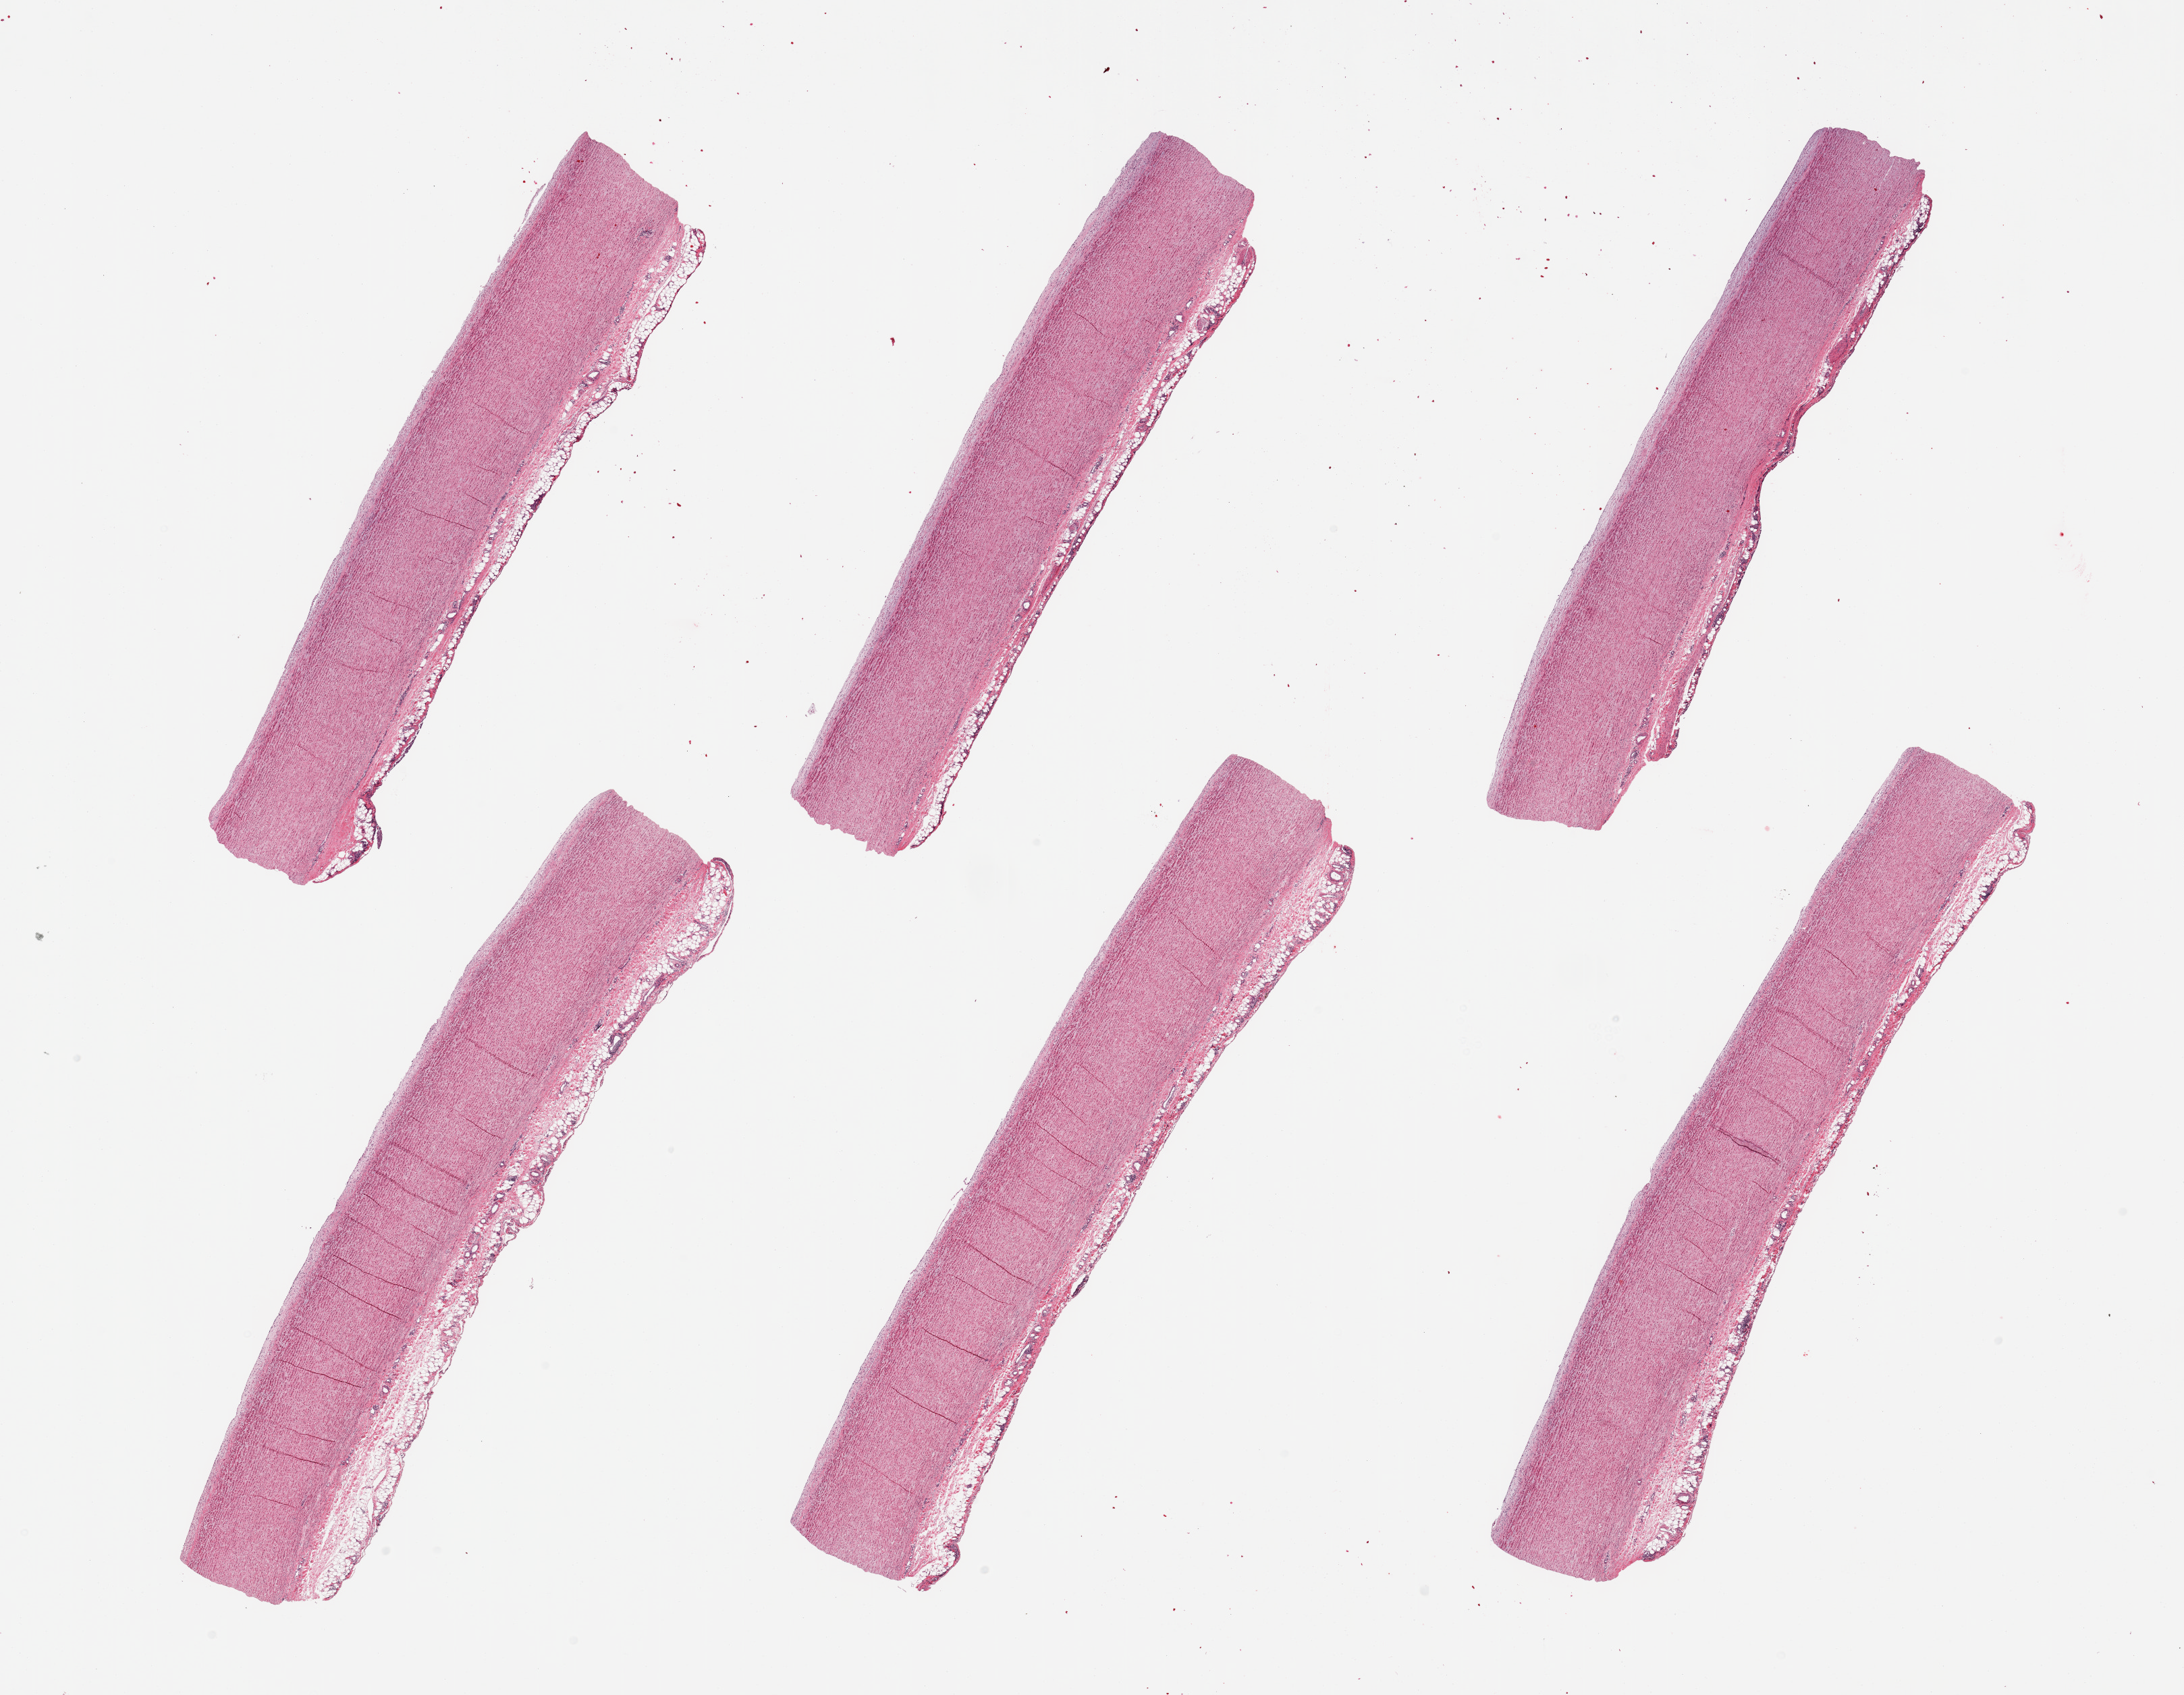
Digitized H&E-stained section, whole scanned area (about 25.6 x 19.9 mm) shown as a low-resolution overview. PAXgene-fixed, paraffin-embedded tissue. Sampled site (target tissue): aorta. Donor tissue sample. Donor: male.
• pathologist's review note for this sample: 6 pieces; mild atherosclerosis